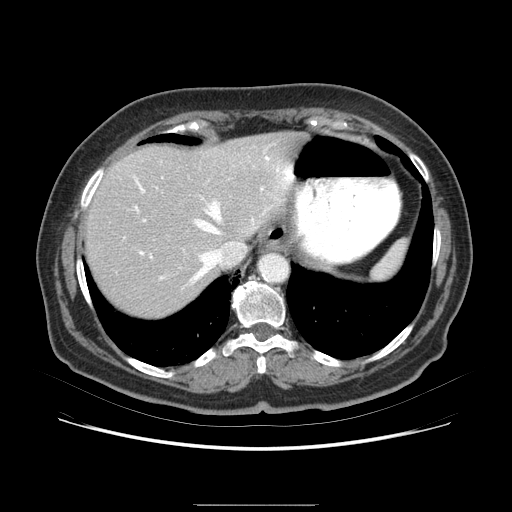
Contrast-enhanced abdominal CT (liver protocol), one axial slice. Position 64 of 79 along the scan axis. Soft-tissue window (W 400 / L 40 HU). 2.5 mm slice thickness. 512 × 512 image matrix. From the clinical record (not read from this slice): diagnosis: hepatocellular carcinoma (patient treated with transarterial chemoembolisation; whether this scan precedes or follows treatment is not stated here); TNM stage (as recorded): Stage-I; Child-Pugh class: A; tumour differentiation: poorly differentiated.
Annotated regions visible in this slice (semi-automatic segmentation, software-assisted and operator-edited):
- liver parenchyma outside the tumour (the mass and vessels are separate outlines, so this box may not span the whole liver): bounding box (x1, y1, x2, y2) in pixels: (90, 140, 318, 296)
- liver vessels: (135, 182, 306, 263)